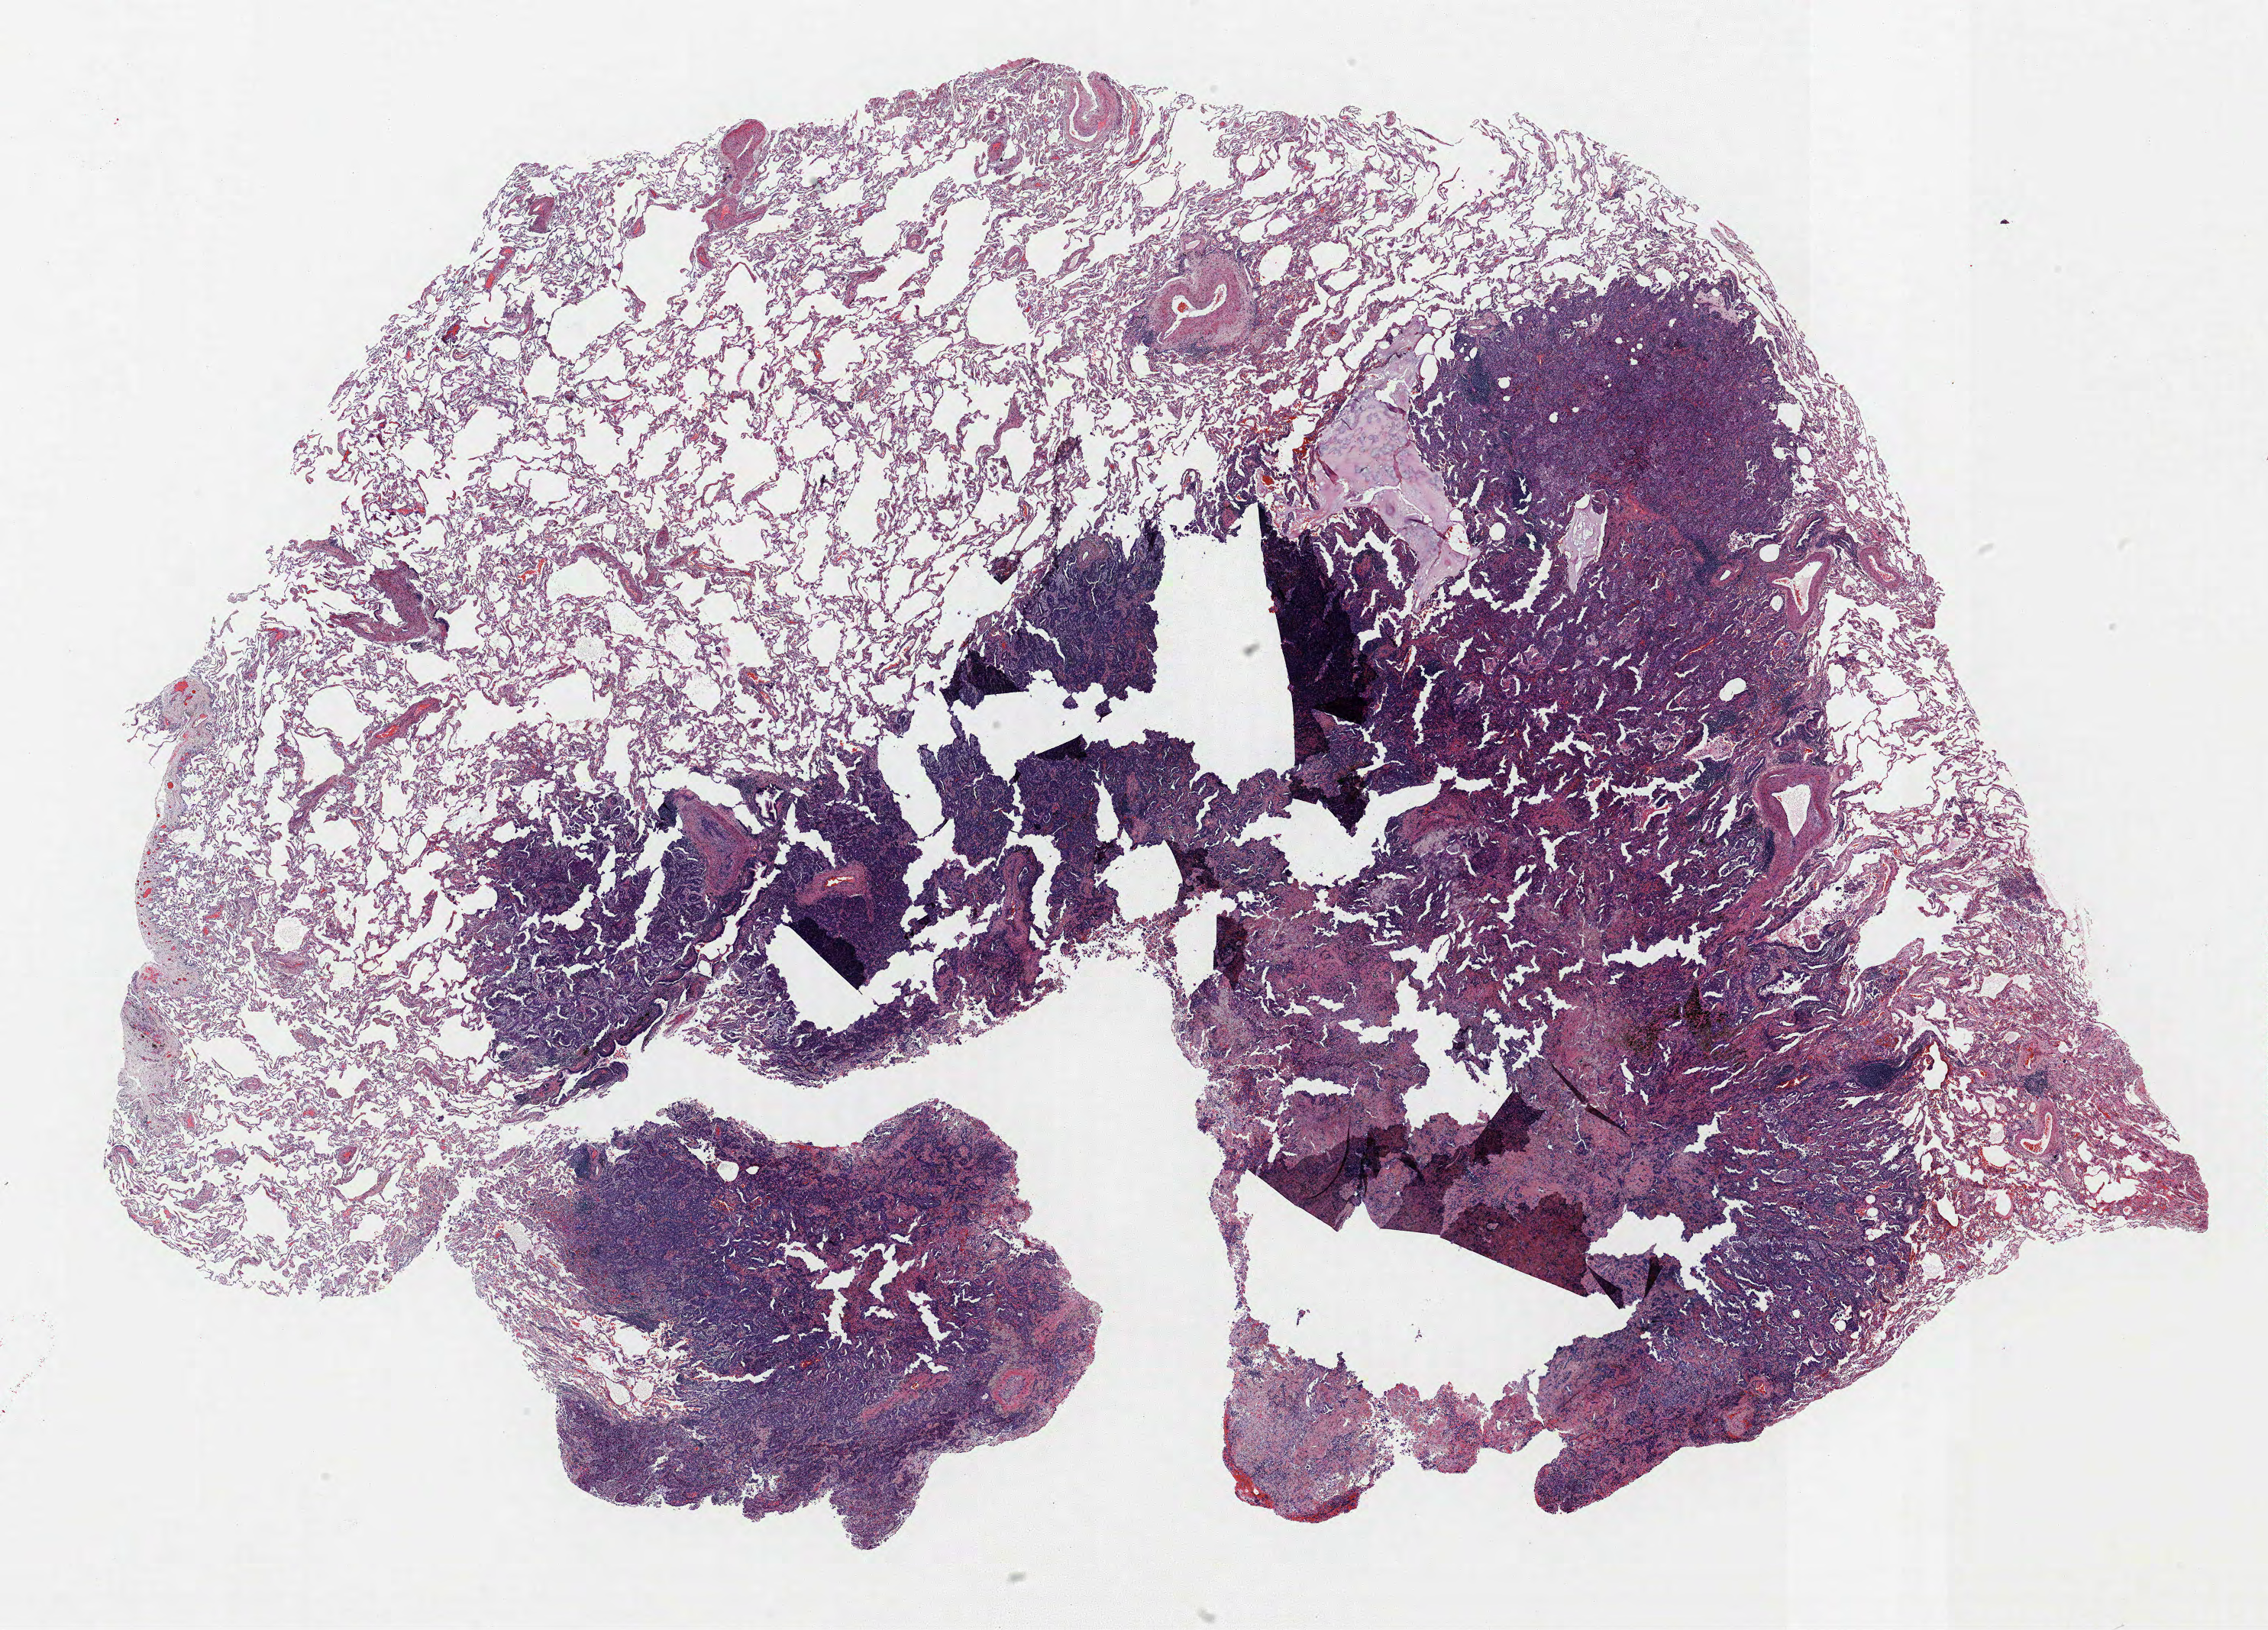
Hematoxylin and eosin (H&E) stained whole-slide image — whole scanned area (about 23.8 x 17.1 mm) shown as a low-resolution overview. Formalin-fixed paraffin-embedded (FFPE) section. Lung. Female patient, aged 72 at enrolment. Former smoker at enrolment. Grade: moderately differentiated (G2).
- primary tumour location (clinical record): right upper lobe
- tumour size (pathology): 15 mm
- participant's lung-cancer diagnosis: Adenocarcinoma, NOS
- ICD-O-3 topography: upper lobe of lung (C34.1)
- stage (AJCC 6th edition): IA